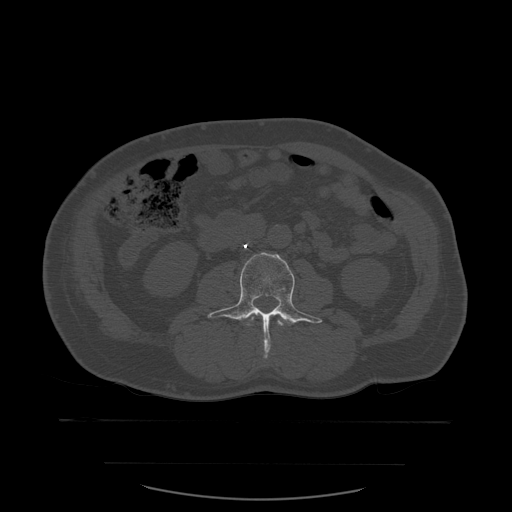
CT including the spine, one axial slice; slice 196 of 590 in the series (ordered by position); bone window (W 1800 / L 400 HU); 1.25 mm slice thickness; 512 × 512 image matrix, field of view 479 × 479 mm. Patient age 71 years. From the clinical record (not read from this slice): primary cancer: lung; vertebrae with lytic lesions (as recorded): T1, T2, L5, S1.
Annotated regions visible in this slice (semi-automatic segmentation, software-assisted and operator-edited):
- L2 vertebra: bounding box <247,313,285,358> (left, top, right, bottom; pixels)
- L3 vertebra: <208,252,323,358>